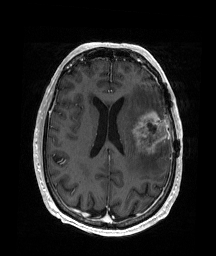
Brain MRI from a brain-tumour surgery series, one axial slice. Position 77 of 176 along the scan axis. T1-weighted post-contrast. 216 × 256 image matrix, field of view 219 × 260 mm. Case-level facts recorded for this patient, not image findings: histopathology: Glioblastoma; WHO grade: 4; IDH mutation: no; tumour location: Left Frontal.
Outlined on this slice (expert manual segmentation):
- tumour: box from (x=132, y=110) to (x=169, y=155) px